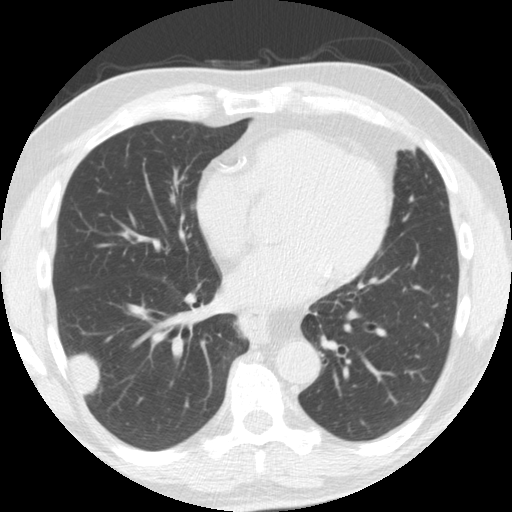
Low-dose screening chest CT, one axial slice; position 74 of 174 along the scan axis; lung window (W 1500 / L -600 HU); 2.5 mm slice thickness; 512 × 512 image matrix.
Structures marked on this image (manually delineated by an expert):
- lesion 1 (tumor, lower lobe of right lung): bounding box (x1, y1, x2, y2) in pixels: (70, 353, 100, 395)